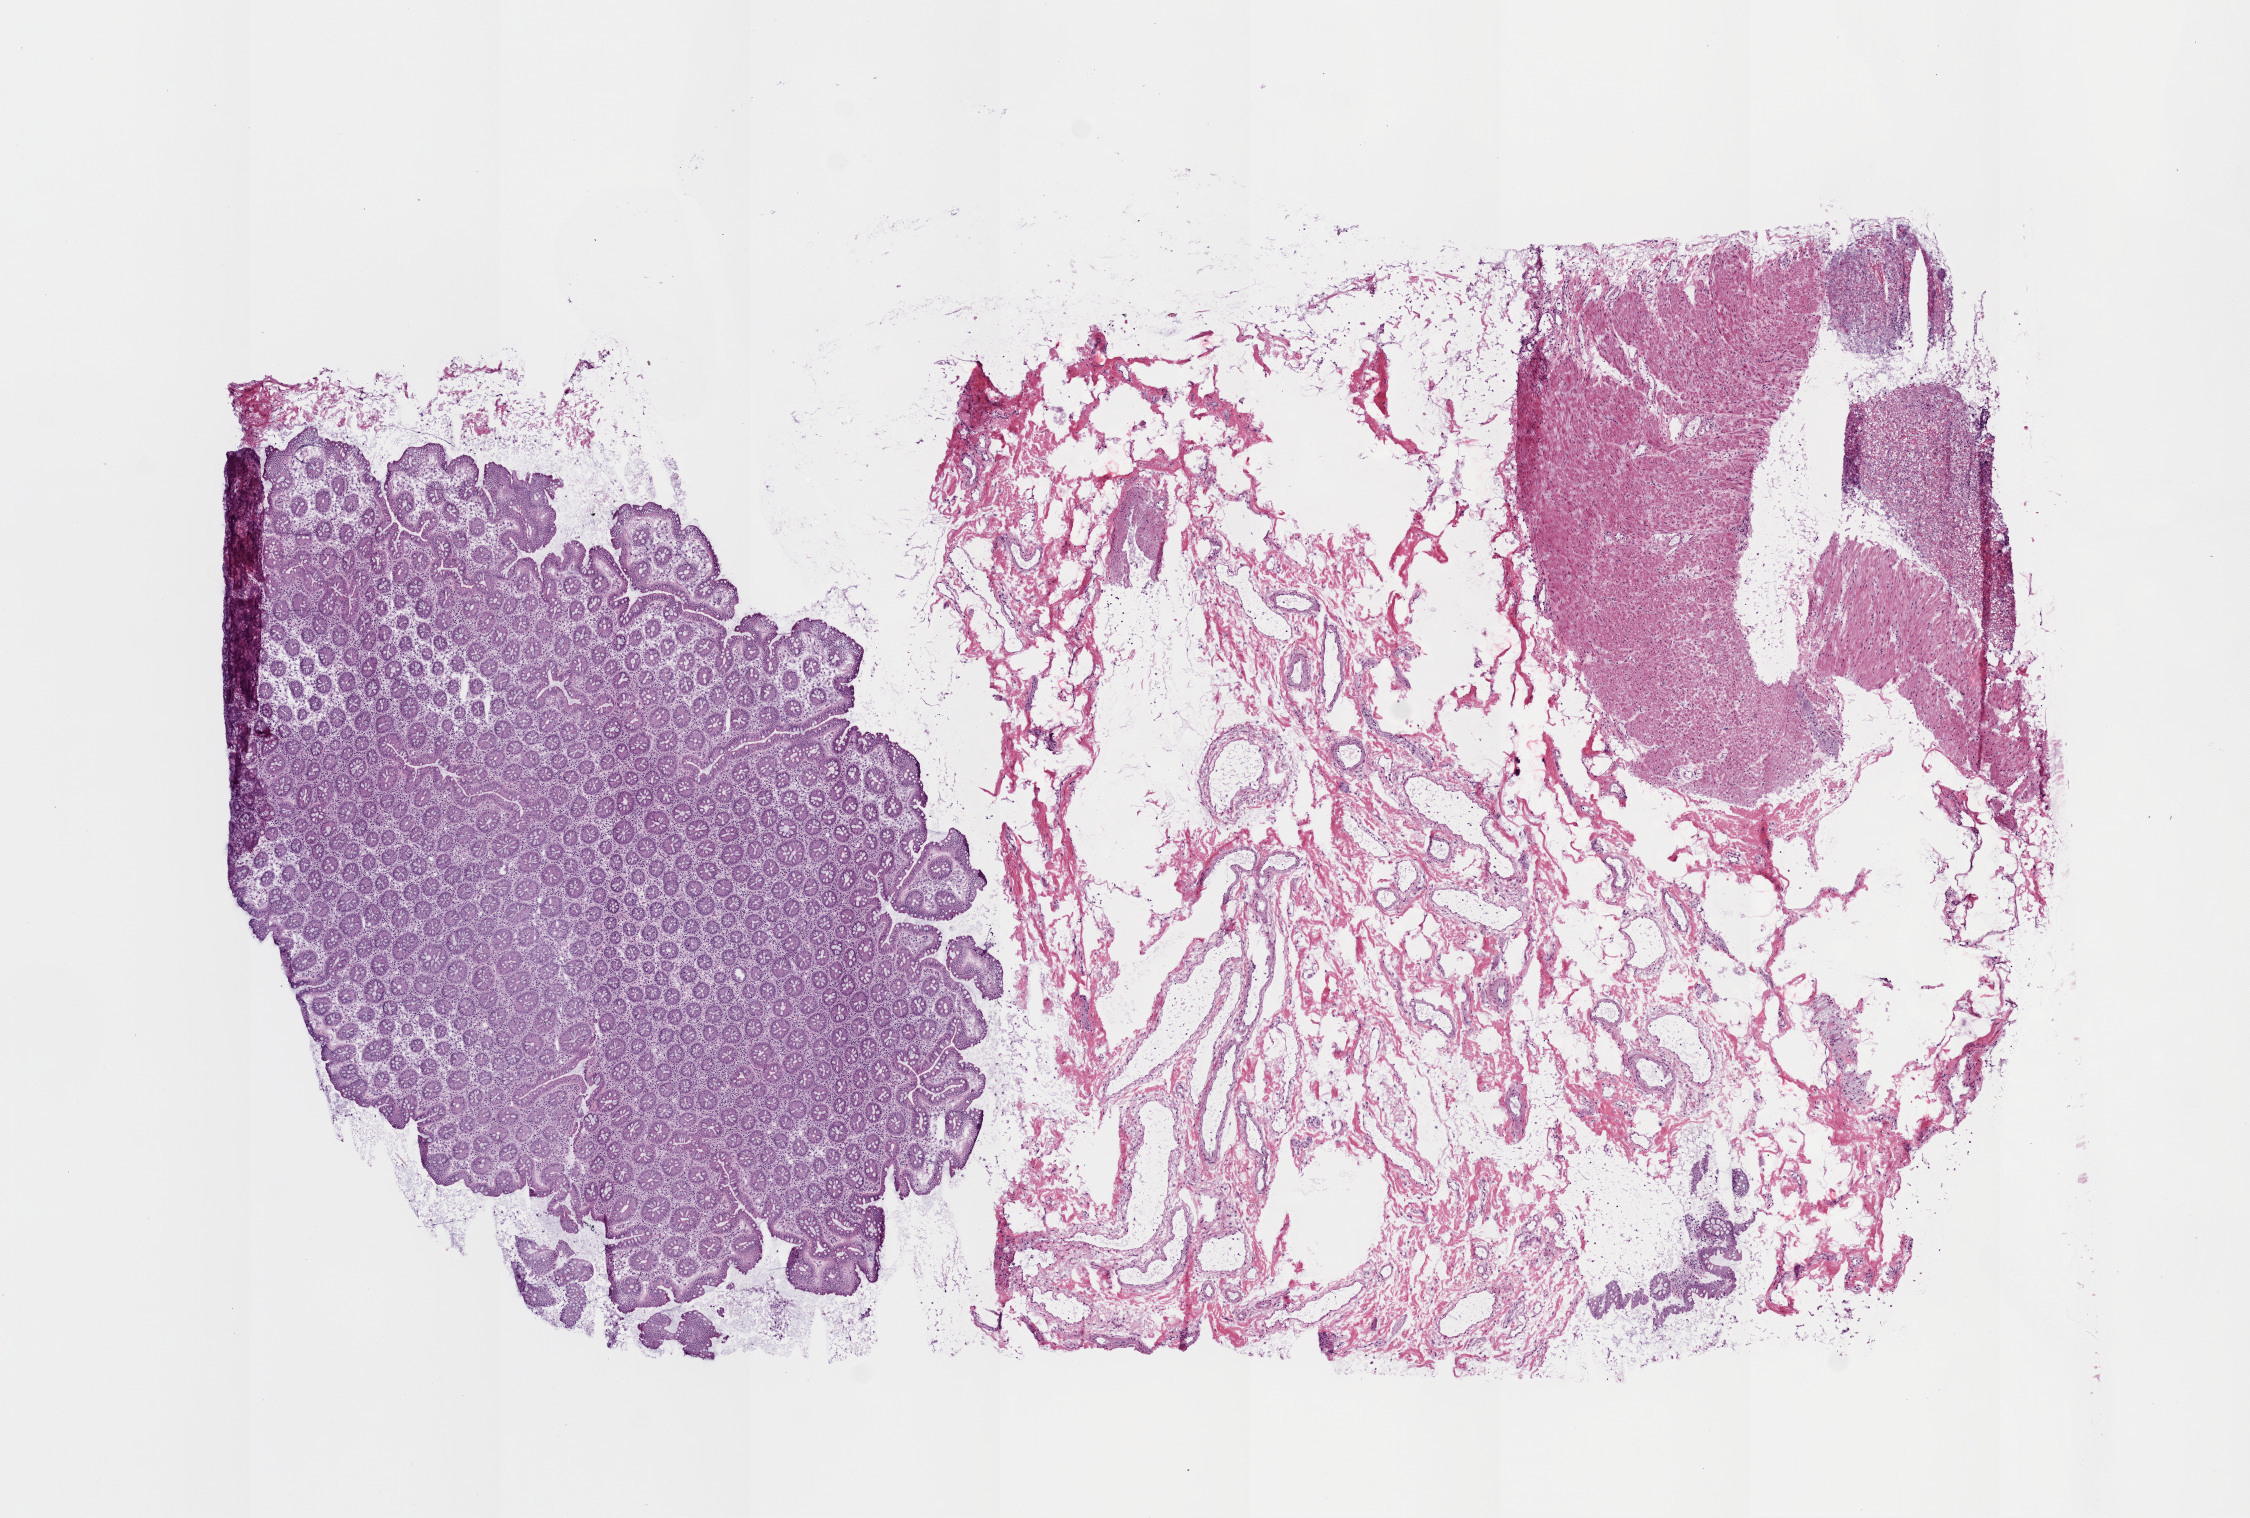
Digitized H&E-stained tissue section (whole slide) — whole scanned area (about 9.0 x 6.1 mm, from a 20x scan) shown as a low-resolution overview; frozen section; solid tissue normal (non-tumour tissue) sample from the colon. Female, age 81 years at initial diagnosis.
- this section: solid tissue normal (non-tumour) sample from the same patient
- patient diagnosis: Adenocarcinoma, NOS